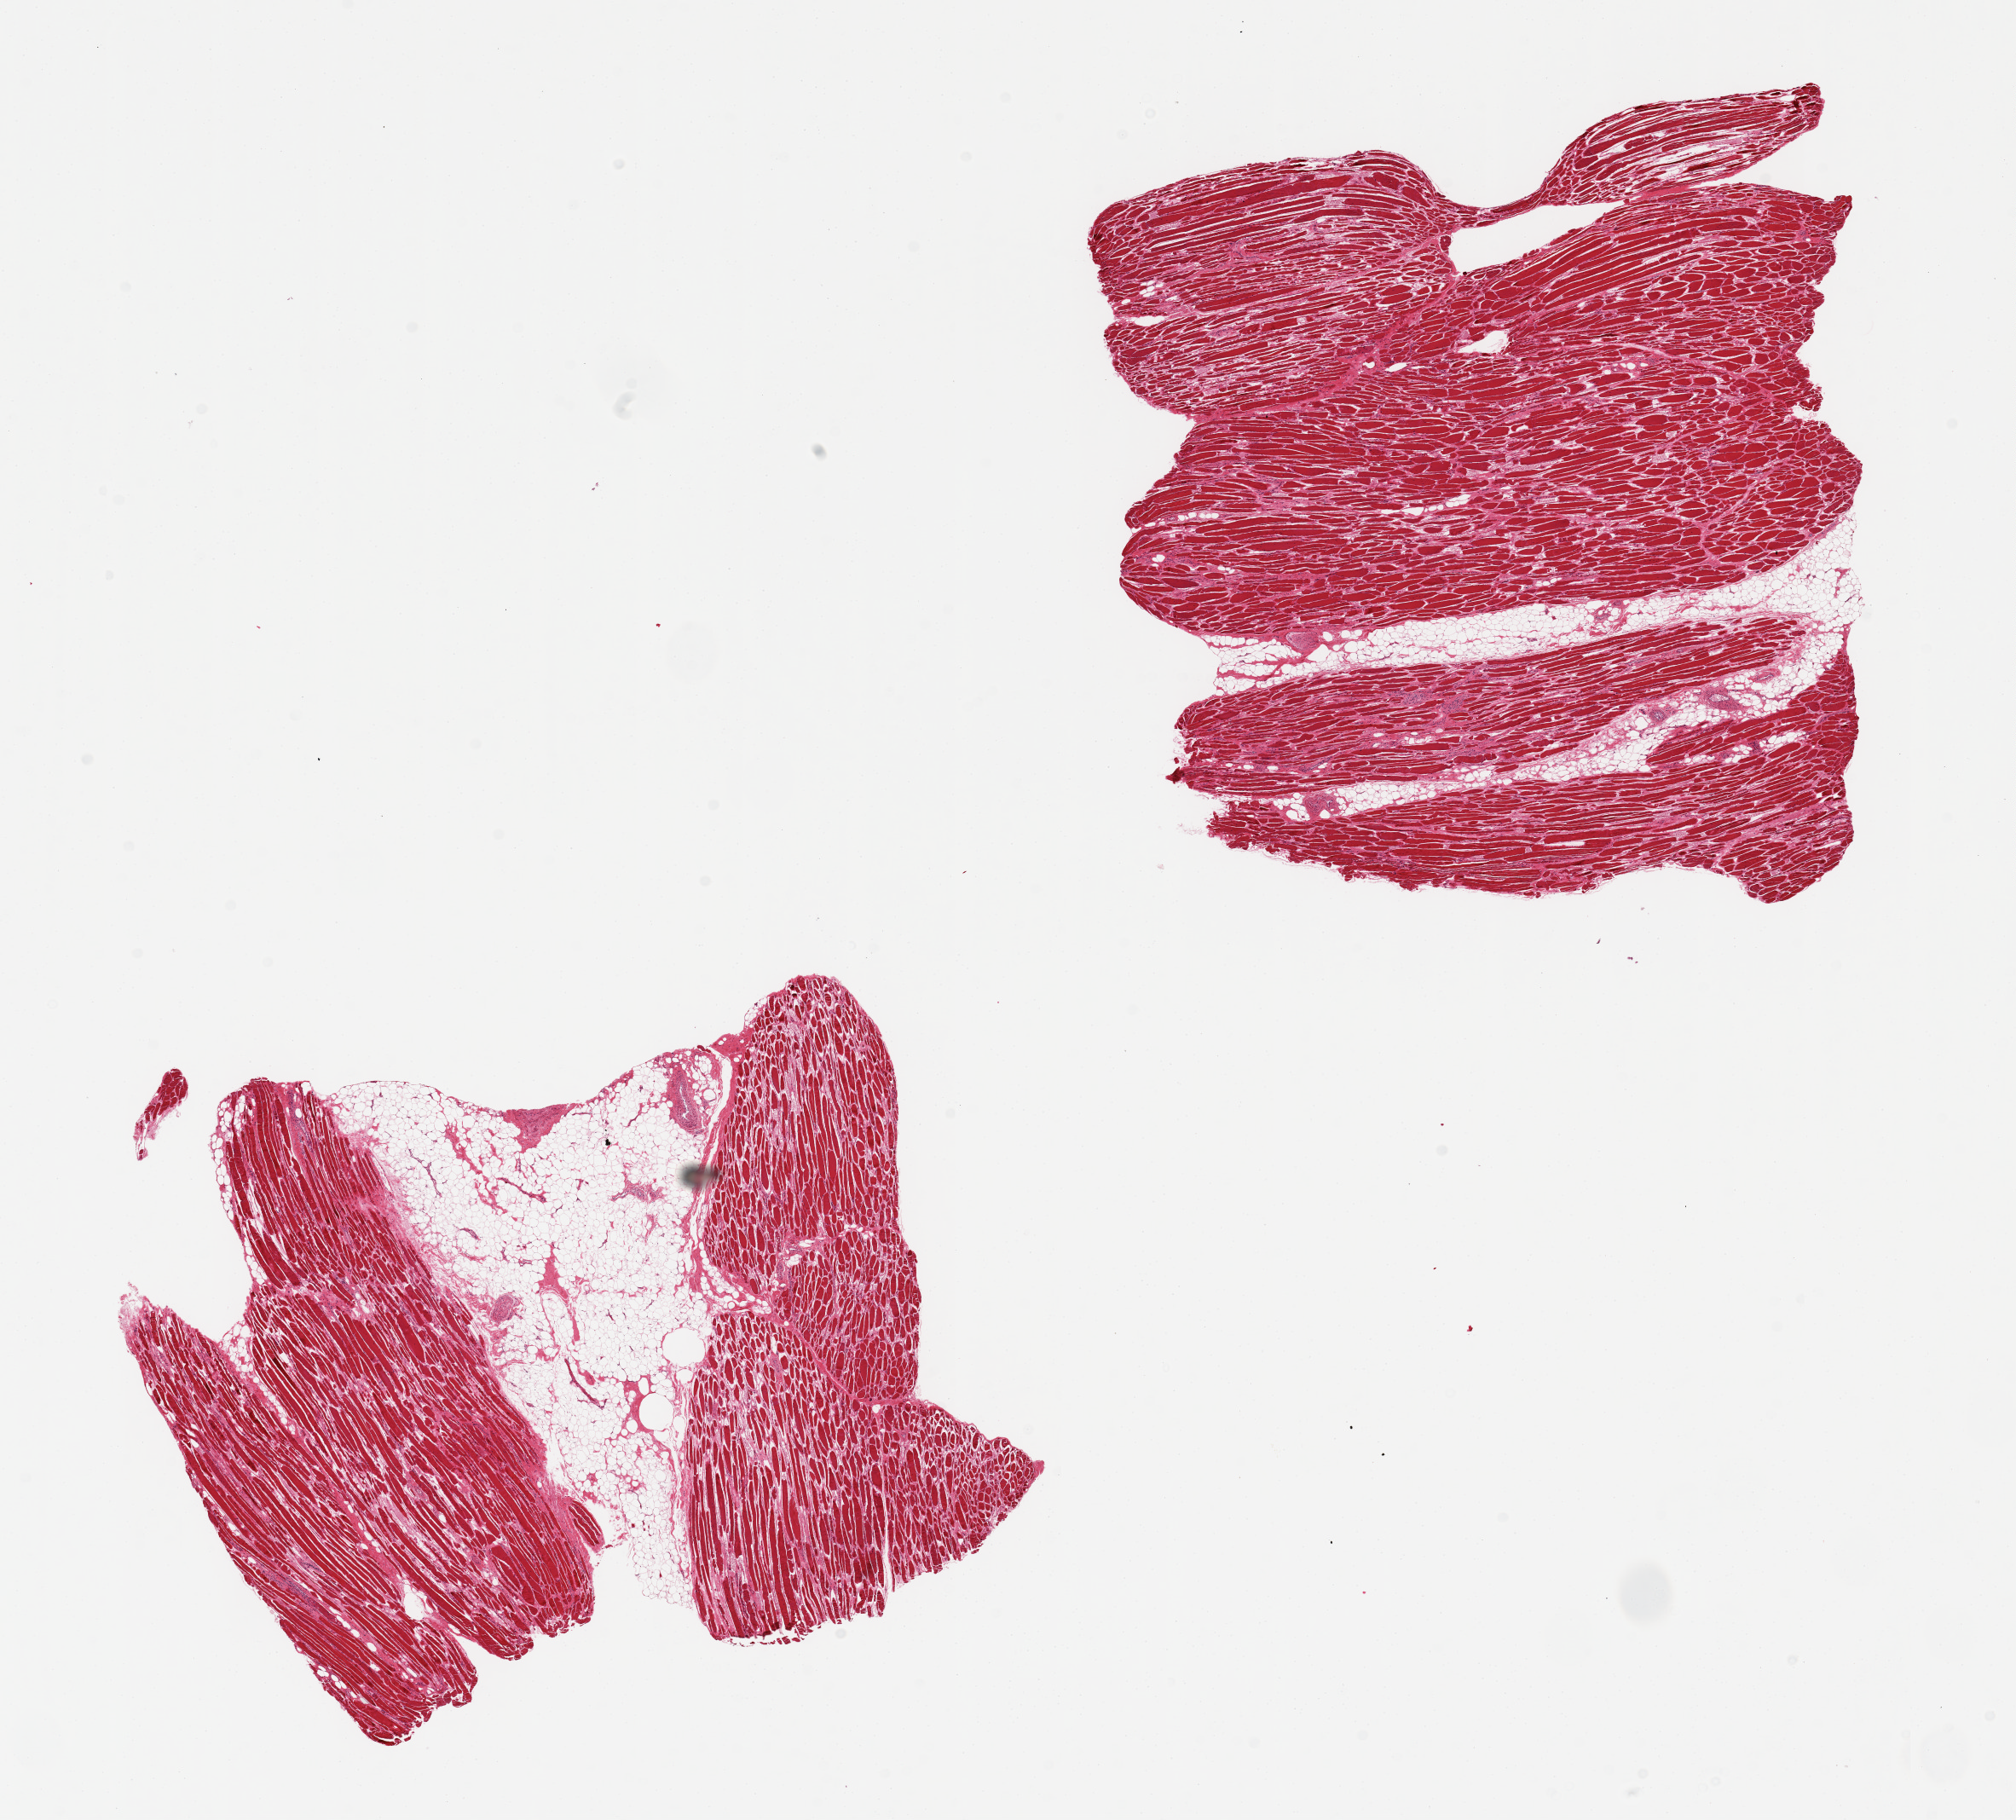
Digitized hematoxylin and eosin (H&E)-stained section, a low-resolution overview of the entire scanned area, about 18.7 x 16.9 mm (from a 20x scan), PAXgene-fixed paraffin-embedded (PFPE) section, target tissue: skeletal muscle, donor tissue sample. Donor sex: female.
Pathologist's review note for this sample: 2 pieces; one has 2 mm, 40%, fat between two muscle bundles.